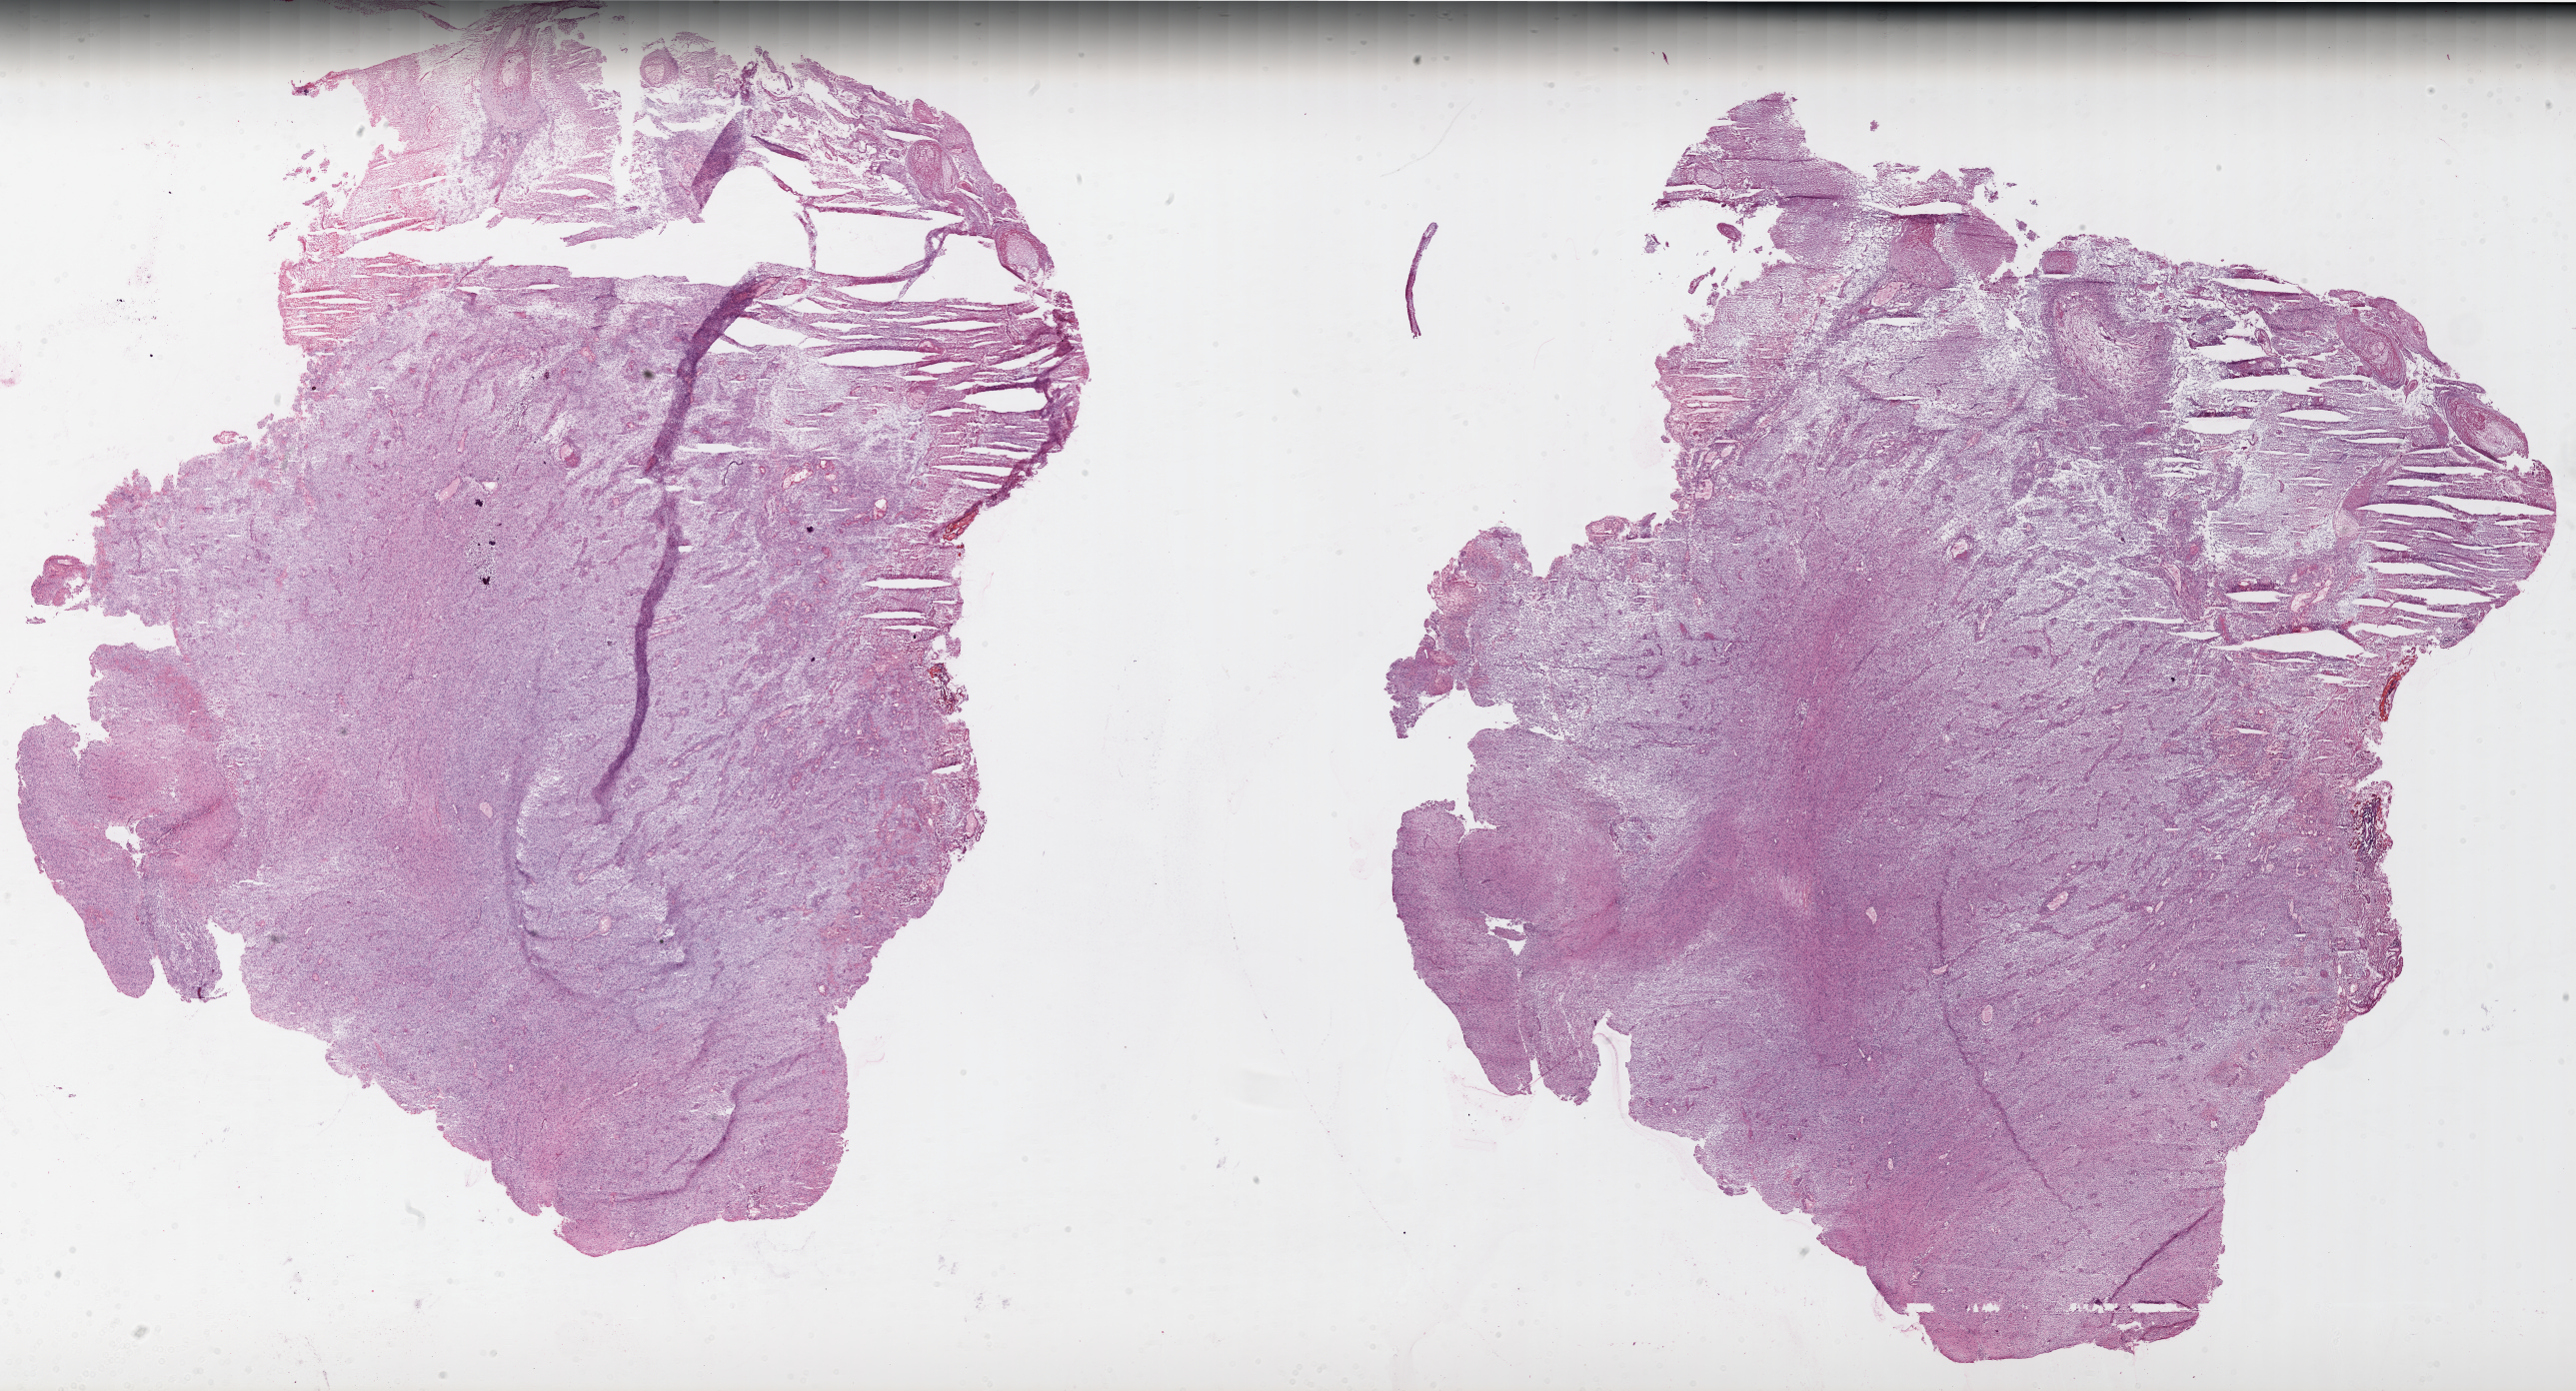
Digitized H&E tissue section (whole slide), whole scanned area (about 41.5 x 22.4 mm) shown as a low-resolution overview, frozen section from the top of the tissue portion, primary tumour sample from the brain. Female patient; age at initial diagnosis 33 years. Composition of this section per pathologist review: tumour cells 80%, tumour nuclei 100%, normal cells 0%, stromal cells 0%, necrosis 20%.
Diagnosis: Glioblastoma.